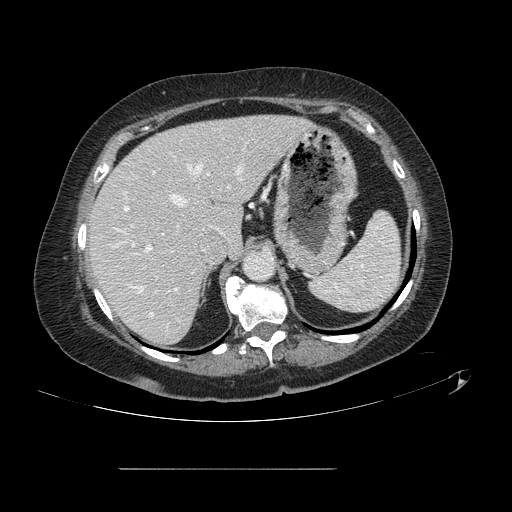
Contrast-enhanced abdominal CT, one axial slice. 120 kVp. Intravenous contrast given. Soft-tissue window (W 400 / L 40 HU). 512 × 512 image matrix, field of view 439 × 439 mm. Female patient, age 75 years. Case-level facts recorded for this patient, not image findings: diagnosis: colorectal cancer liver metastases, imaged before liver resection; multiple liver metastases: no; largest metastasis: 2.4 cm.
Structures marked on this image (manually delineated by an expert):
- hepatic veins: box from (x=135, y=166) to (x=244, y=316) px
- liver: (x=90, y=116)–(x=309, y=345)
- planned liver remnant (the part of the liver to remain after resection): (x=90, y=116)–(x=308, y=345)
- portal vein (with intrahepatic branches): (x=124, y=142)–(x=247, y=291)